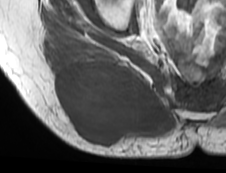
MRI of an extremity soft-tissue mass, one axial slice. Position 36 of 73 along the scan axis. MR volume resampled by the dataset authors to the PET/CT grid (not the native acquisition matrix). 226 × 173 image matrix, field of view 221 × 169 mm. Female patient. Case-level facts recorded for this patient, not image findings: histological type: spindle cell suggestive of myxofibrosarcoma; grade: intermediate; site of the primary tumour: right buttock.
Structures marked on this image (expert contour drawn on MRI and transferred to this co-registered scan by the dataset authors):
- gross tumour volume (mass): bounding box <52,58,165,144> (left, top, right, bottom; pixels)